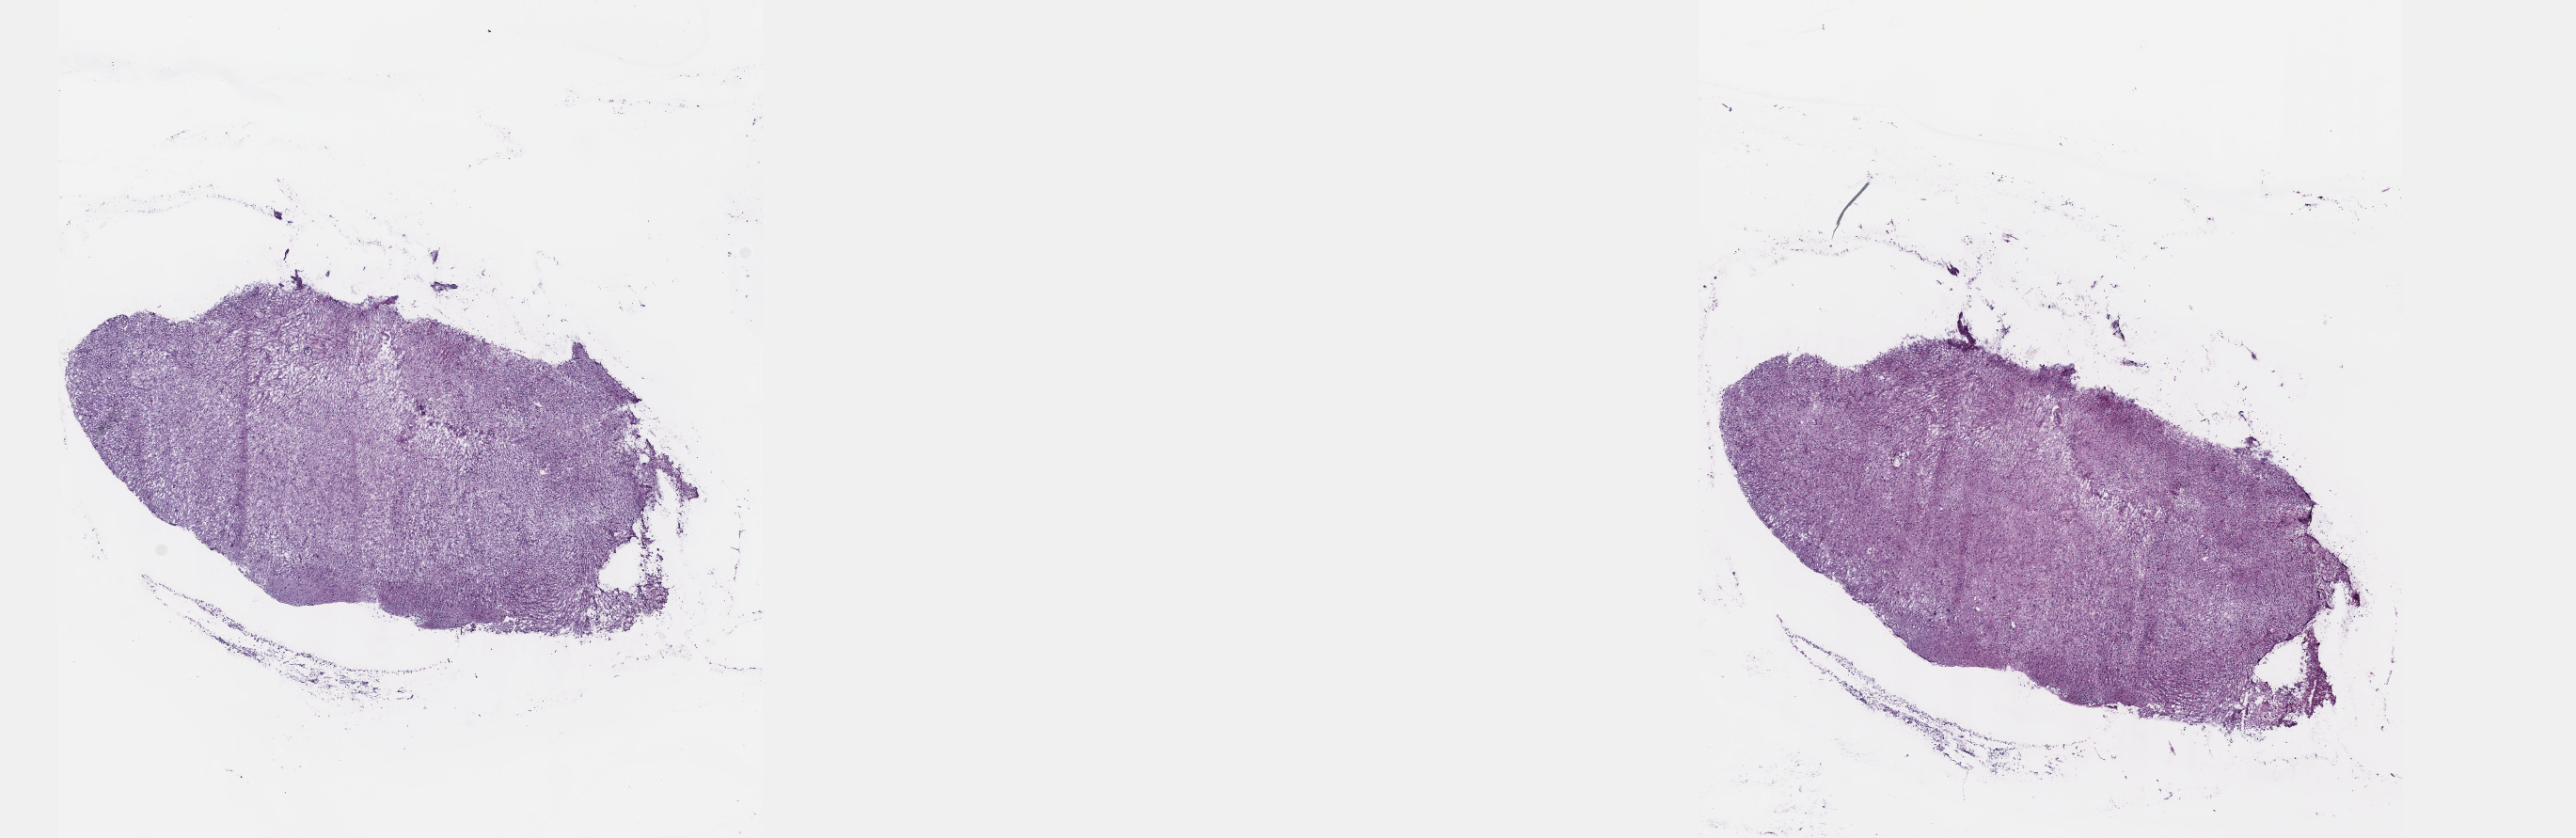
H&E-stained whole-slide image, low-resolution overview of the scanned area, about 22.1 x 7.2 mm. Frozen section from the top of the tissue portion. Primary tumour sample from the brain. Male, age 33 years at initial diagnosis. Histologic grade: G2 (moderately differentiated). Pathologist review of this section (percent, as recorded): tumour cells 30%, tumour nuclei 80%, normal cells 10%, stromal cells 60%, necrosis 0%. Inflammatory infiltration, as recorded: lymphocyte infiltration 0%, monocyte infiltration 0%, neutrophil infiltration 0%.
- pathologic diagnosis: Oligodendroglioma, NOS
- laterality: left